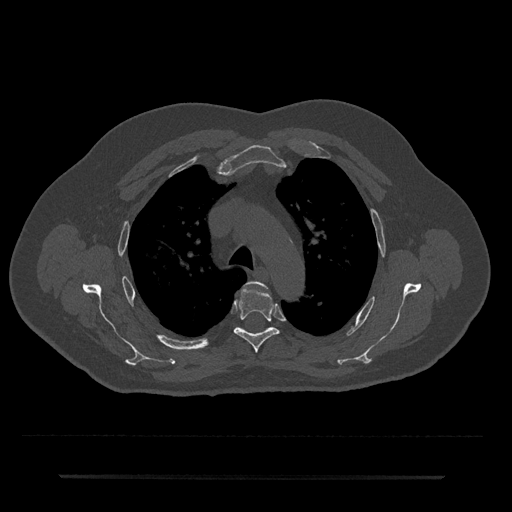
CT including the spine, one axial slice. Slice 526 of 797 in the series (ordered by position). Reconstruction kernel Br40s/3. 120 kVp. Bone window (W 1800 / L 400 HU). 0.5 mm slice thickness. 512 × 512 image matrix, field of view 437 × 437 mm. Patient: male, 69 years. From the clinical record (not read from this slice): primary cancer: prostate.
Structures marked on this image (semi-automatic segmentation, software-assisted and operator-edited):
- T3 vertebra: bounding box (x1, y1, x2, y2) in pixels: (246, 282, 260, 288)
- T4 vertebra: (234, 288, 279, 353)
- T5 vertebra: (241, 328, 244, 330)